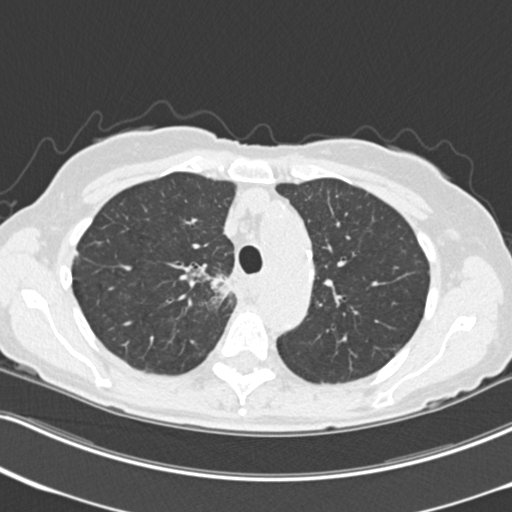
Low-dose screening chest CT, one axial slice; slice 166 of 226 in the series (ordered by position); 120 kVp; lung window (W 1500 / L -600 HU); 2 mm slice thickness; 512 × 512 image matrix, field of view 322 × 322 mm.
Outlined on this slice (outlined manually by an expert reader):
- lesion 1 (tumor, mediastinum): bounding box <211,275,230,299> (left, top, right, bottom; pixels)